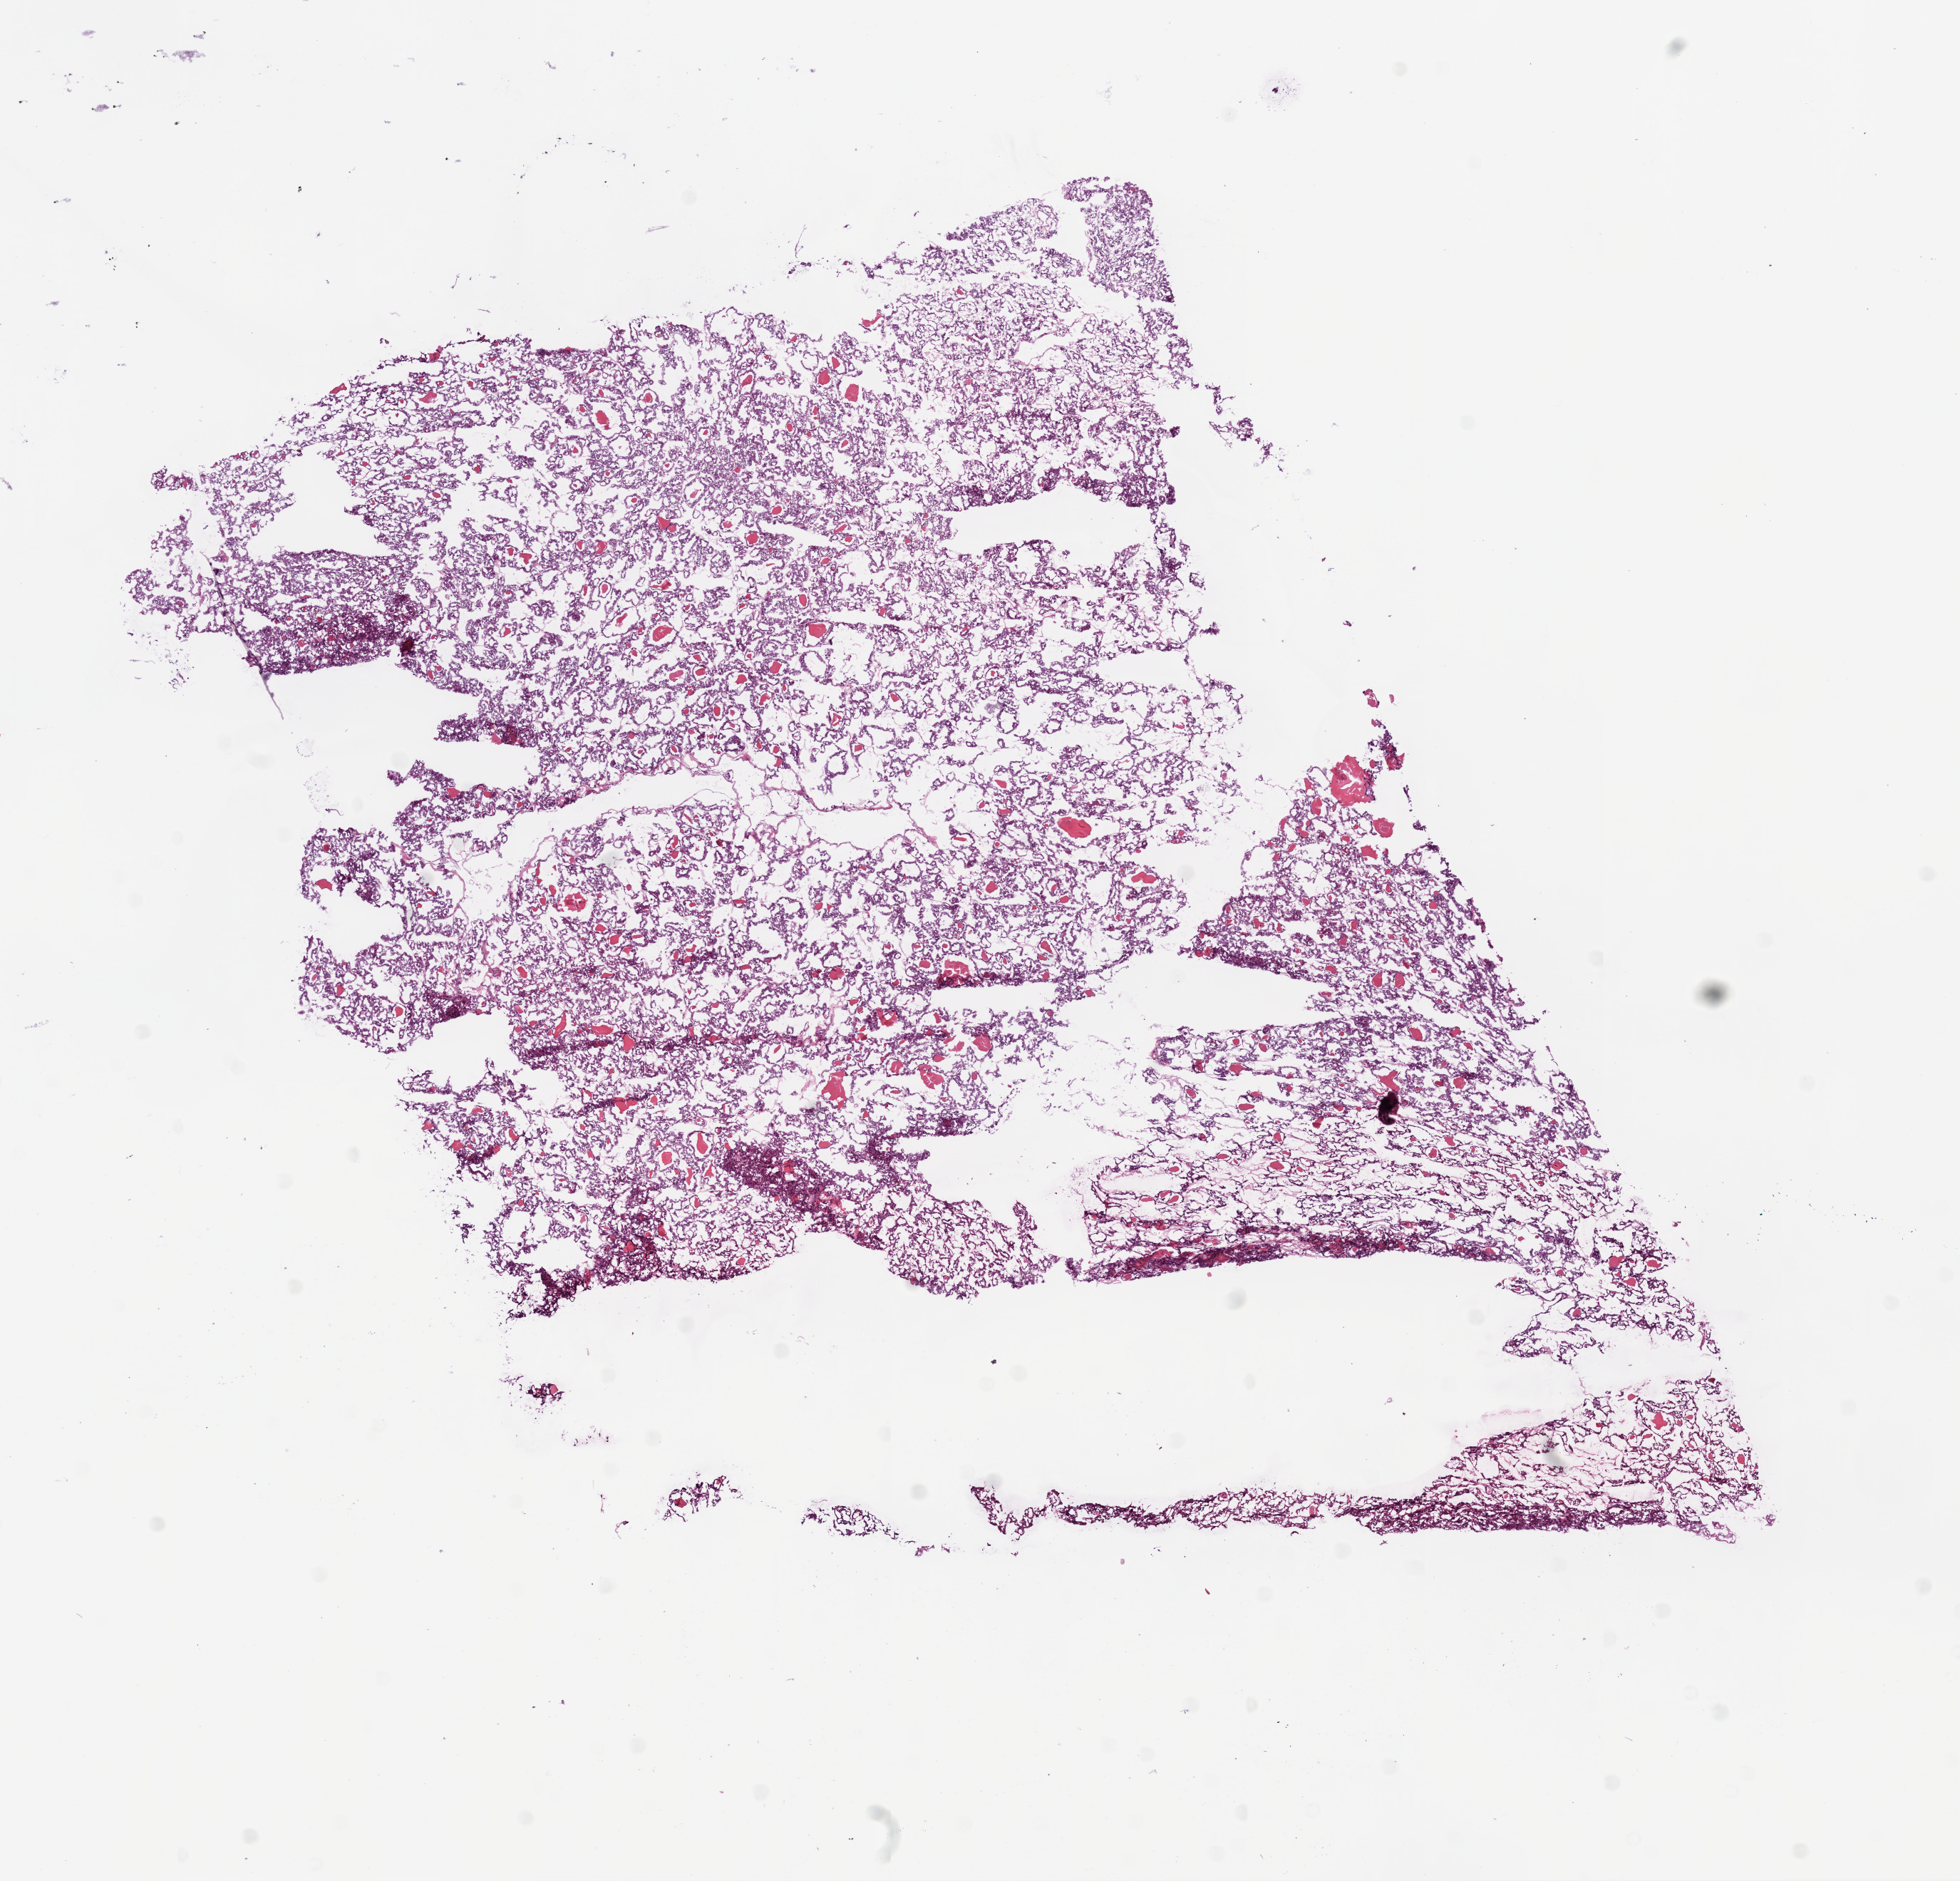
Whole-slide histology image, Hematoxylin and eosin (H&E) stained — shown as a low-resolution overview of the whole scanned area (about 11.0 x 10.6 mm, acquisition: 20x scan), frozen section, sample: primary tumour, kidney. Patient: female, age at initial diagnosis 58 years. Histologic grade: G2 (moderately differentiated). Pathologist review of this section (percent, as recorded): tumour cells 95%, tumour nuclei 85%, normal cells 0%, stromal cells 5%, necrosis 0%.
AJCC pathologic stage: II (6th edition). Pathologic diagnosis: Clear cell adenocarcinoma, NOS.